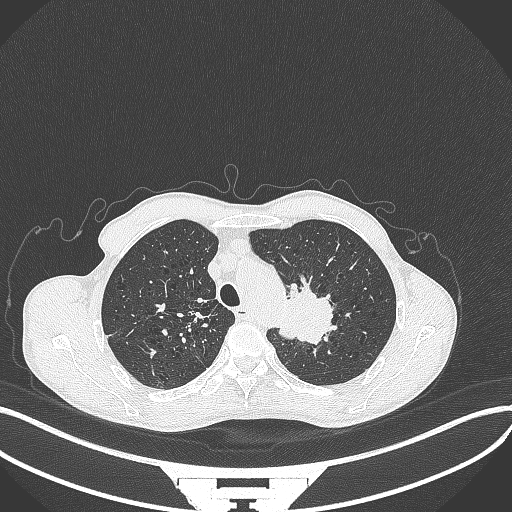
Chest CT, one axial slice. Slice 330 of 386 in the series (ordered by position). Reconstruction kernel B70f. 120 kVp. Lung window (W 1500 / L -600 HU). 1 mm slice thickness. 512 × 512 image matrix. Patient: male, 65 years. Case-level facts recorded for this patient, not image findings: clinical TNM (as recorded): T2b N0 M0; histopathological grade: G2.
Outlined on this slice (bounding box drawn by a radiologist):
- lung tumour (recorded histology: adenocarcinoma): bounding box [x1, y1, x2, y2] px = [279, 279, 336, 346]